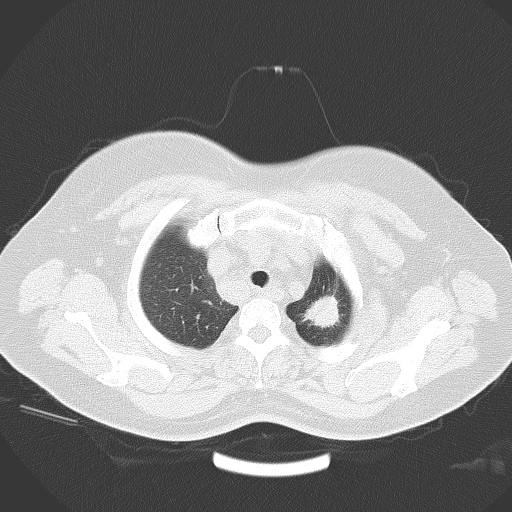
Chest CT, one axial slice; position 51 of 58 along the scan axis; 120 kVp; lung window (W 1500 / L -600 HU); 5 mm slice thickness; 512 × 512 image matrix. Female patient, age 53 years. From the clinical record (not read from this slice): clinical TNM (as recorded): T1c N3 M0.
Outlined on this slice (bounding box drawn by a radiologist):
- lung tumour (recorded histology: adenocarcinoma): box from (x=304, y=289) to (x=342, y=335) px